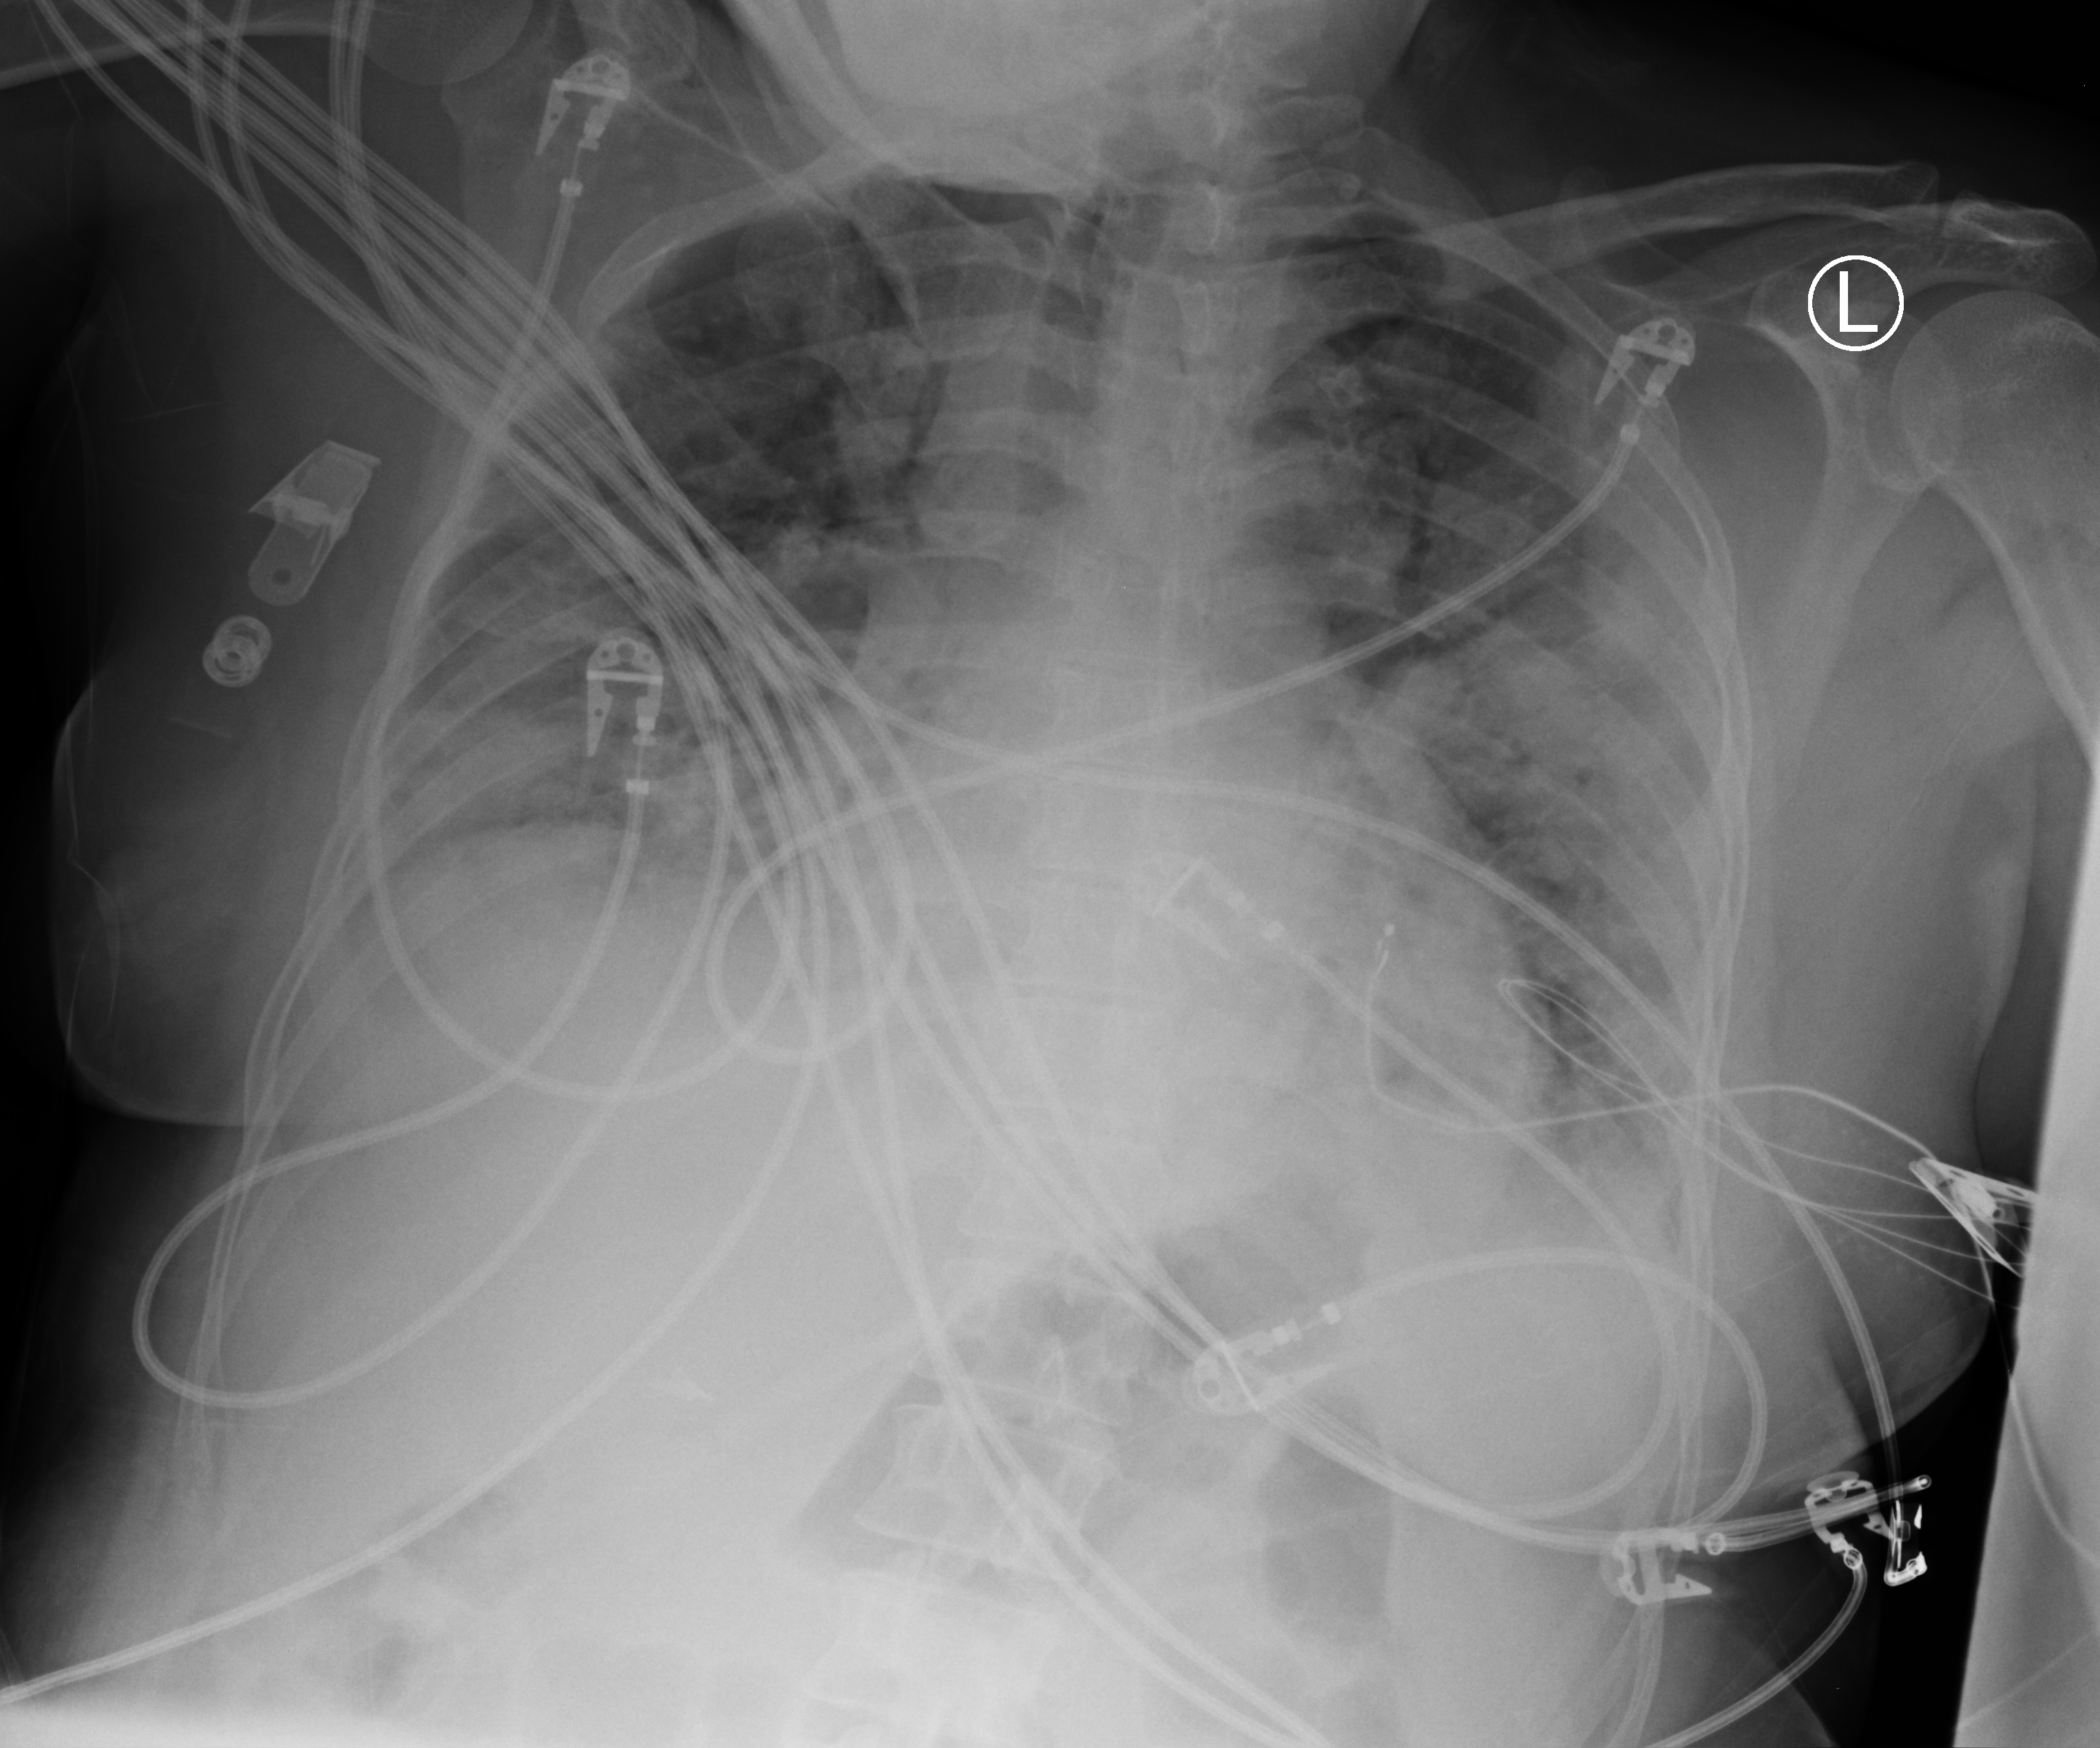
Bedside chest radiograph (computed radiography), anteroposterior (AP) projection. Female patient hospitalised with COVID-19, age 18–59 years.
Admission-level facts for this patient (not findings on this image; timing relative to this image not recorded): mechanically ventilated during this hospital stay: yes; length of hospital stay: 22 days.